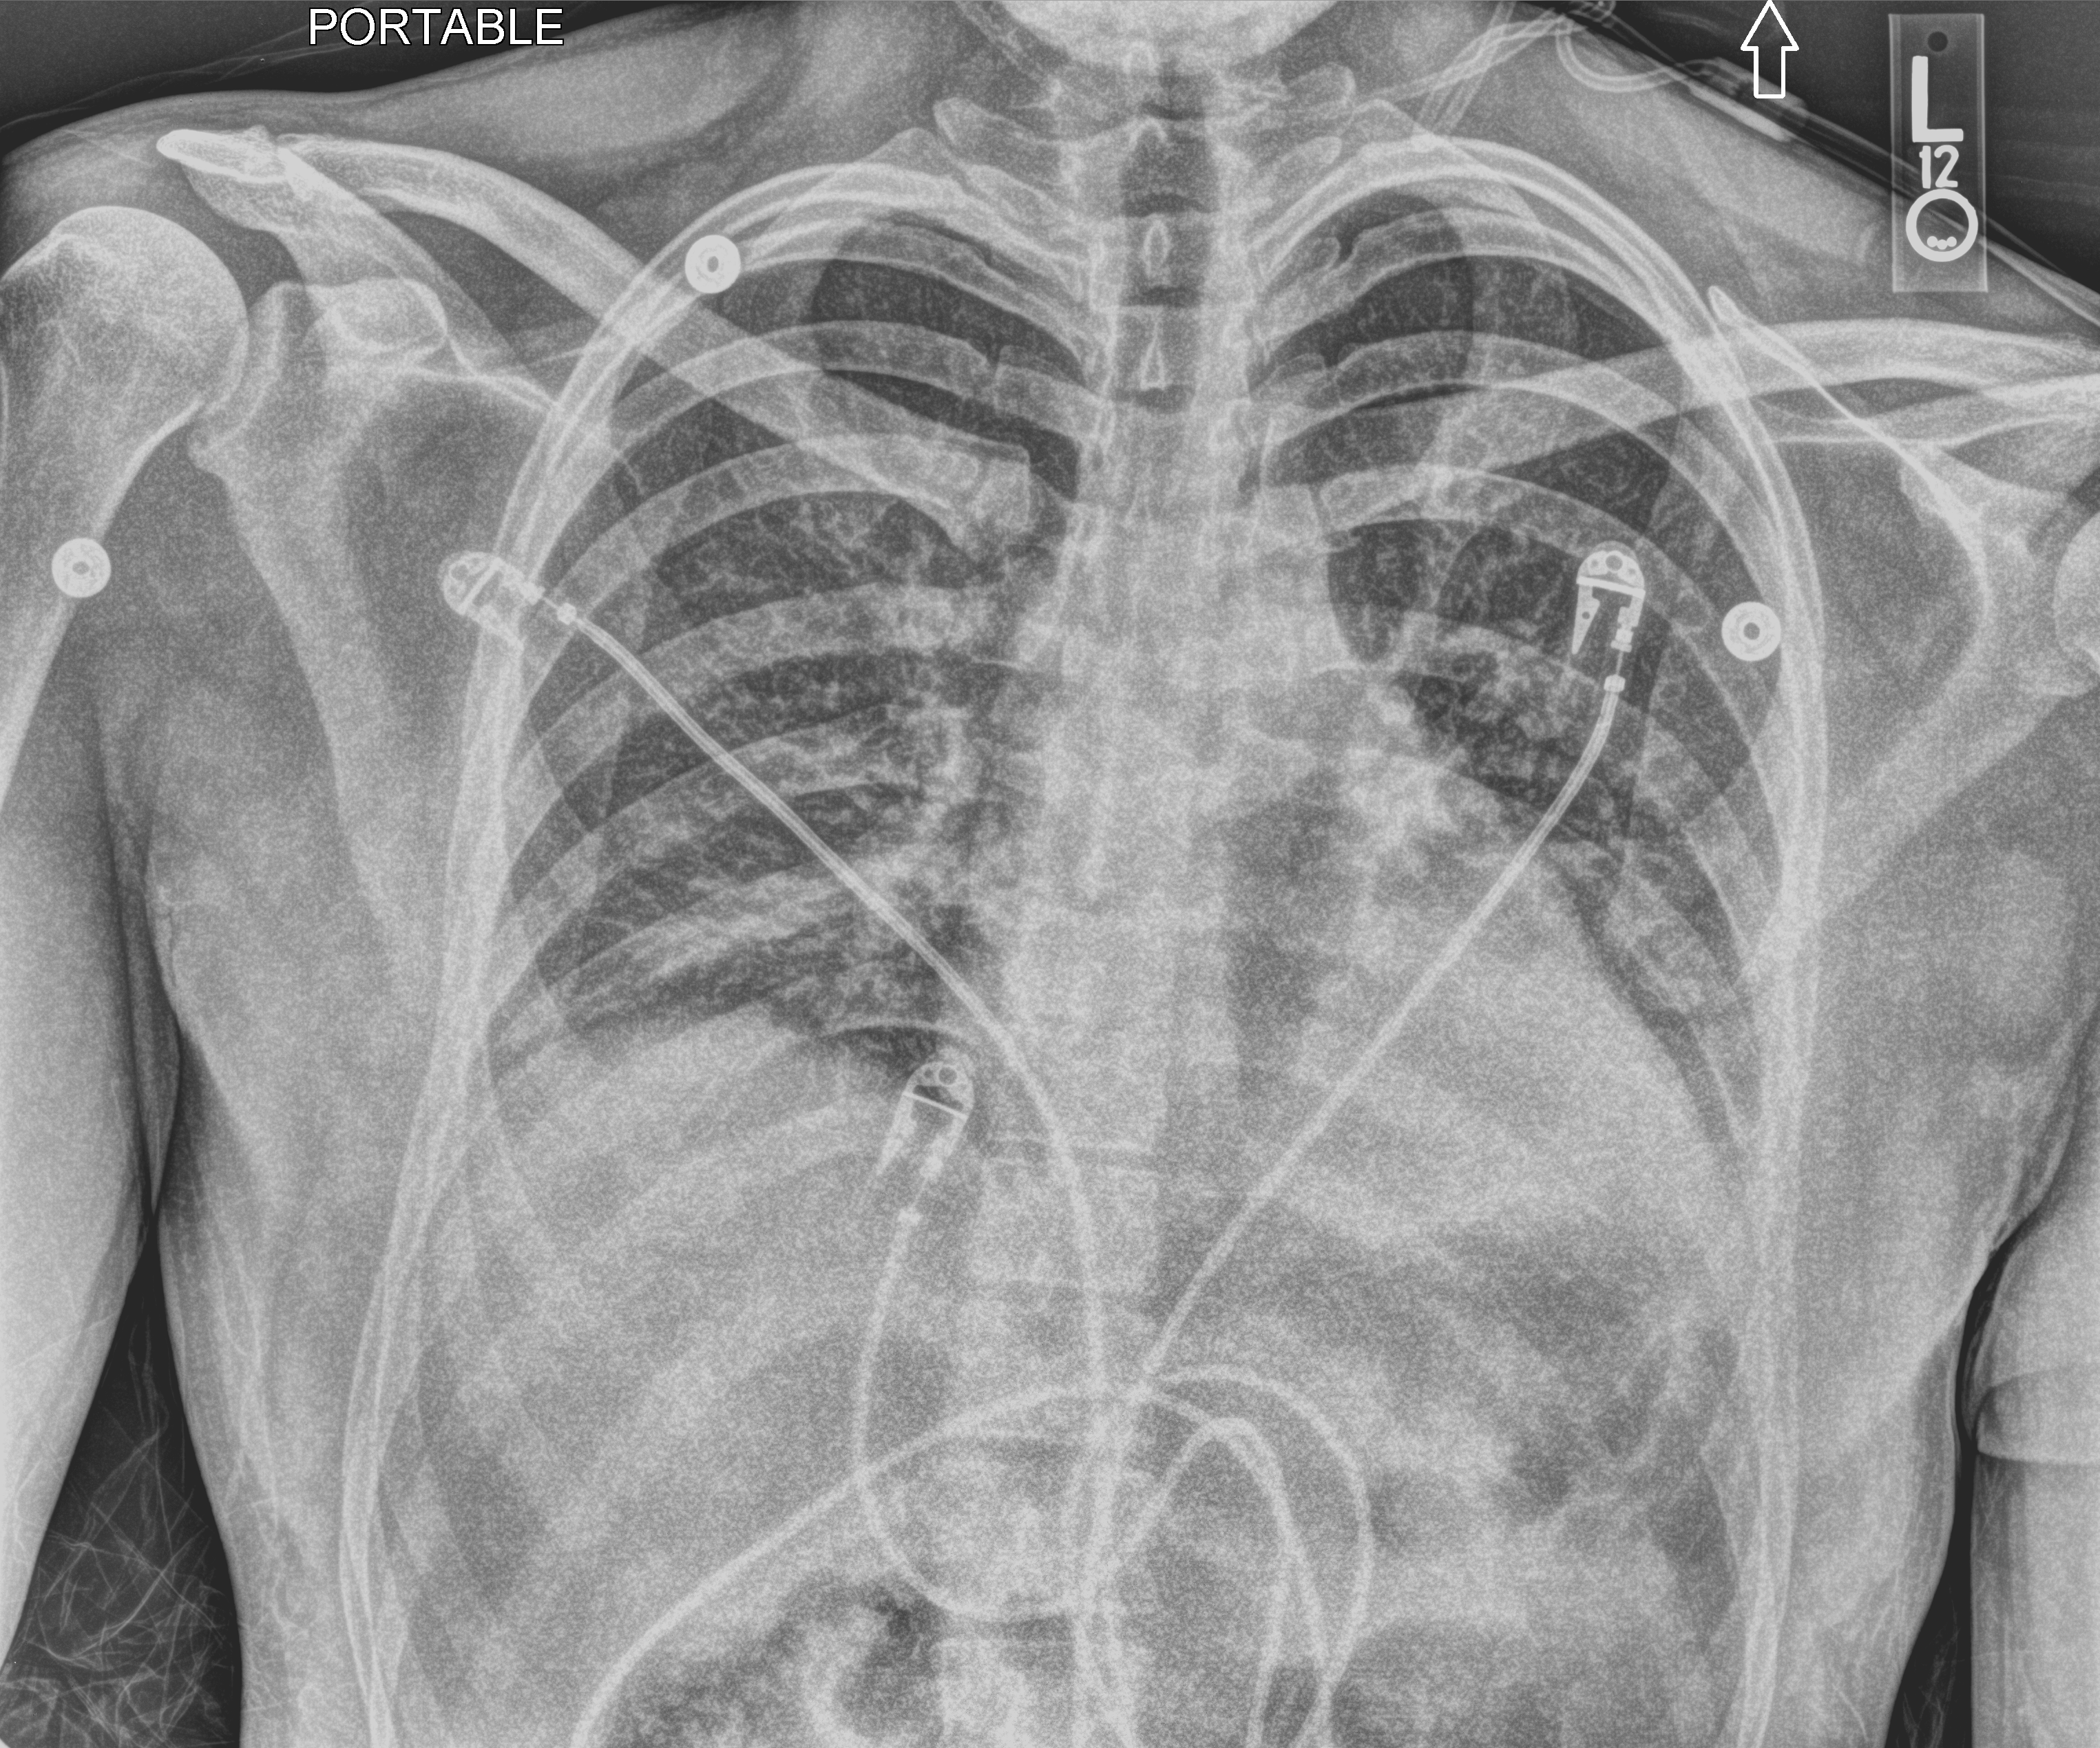
Chest X-ray (portable); anteroposterior (AP) projection. Patient hospitalised with COVID-19; male, aged 18–59 years.
From the hospital-stay record, not from the radiograph (when in the stay this image was taken is not recorded):
- COPD (admission record): no
- mechanically ventilated during this hospital stay: no
- diabetes (admission record): no